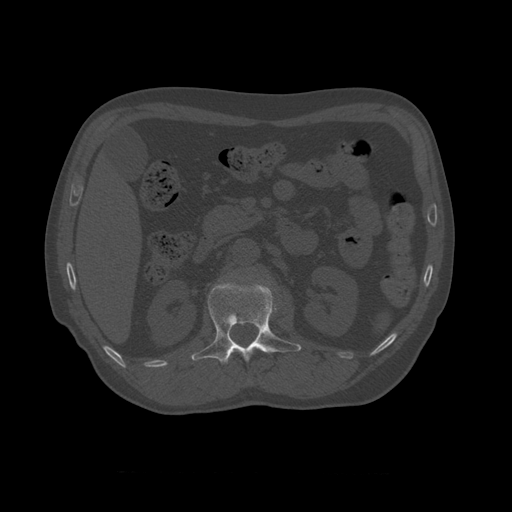
CT including the spine, one axial slice; slice 354 of 450 in the series (ordered by position); reconstruction kernel STANDARD; 120 kVp; bone window (W 1800 / L 400 HU); 1.25 mm slice thickness; 512 × 512 image matrix, field of view 405 × 405 mm. Patient age 75 years. From the clinical record (not read from this slice): primary cancer: prostate.
Outlined on this slice (semi-automatic segmentation, software-assisted and operator-edited):
- L1 vertebra: bounding box [x1, y1, x2, y2] px = [191, 275, 302, 364]
- T11 vertebra: [225, 356, 231, 363]